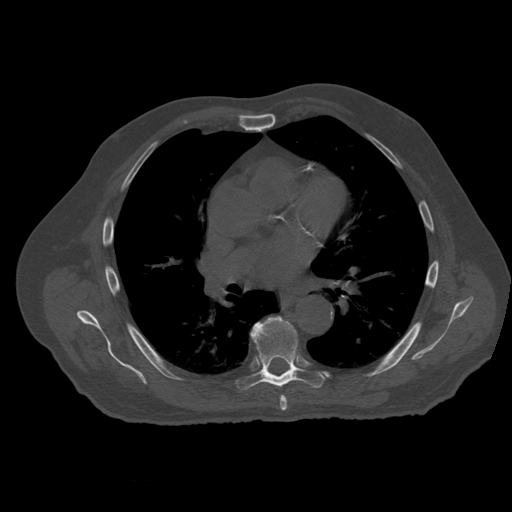
CT including the spine, one axial slice; slice 366 of 399 in the series (ordered by position); reconstruction kernel STANDARD; 120 kVp; bone window (W 1800 / L 400 HU); 1.25 mm slice thickness; 512 × 512 image matrix. Patient age 73 years. Case-level facts recorded for this patient, not image findings: primary cancer: prostate.
Outlined on this slice (semi-automatically segmented with operator editing):
- T6 vertebra: bounding box <280,396,288,412> (left, top, right, bottom; pixels)
- T7 vertebra: <238,317,325,389>